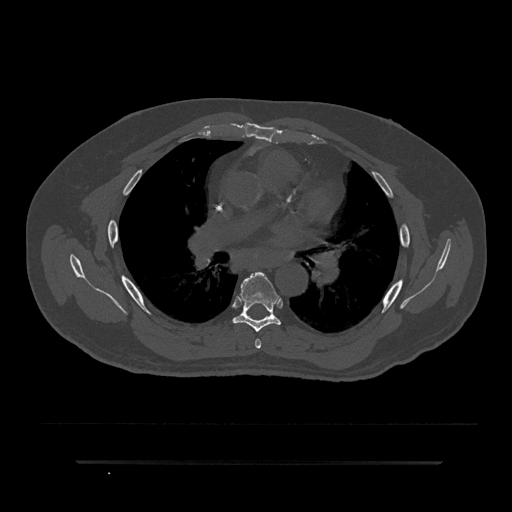
CT including the spine, one axial slice; slice 531 of 797 in the series (ordered by position); reconstruction kernel Br40s/3; bone window (W 1800 / L 400 HU); 0.5 mm slice thickness; 512 × 512 image matrix, field of view 464 × 464 mm. Patient: male, 59 years. From the clinical record (not read from this slice): primary cancer: bile ducts; vertebrae with lytic lesions (as recorded): T10.
Structures marked on this image (semi-automatically segmented with operator editing):
- T5 vertebra: box from (x=255, y=339) to (x=262, y=349) px
- T6 vertebra: (x=232, y=272)–(x=281, y=332)